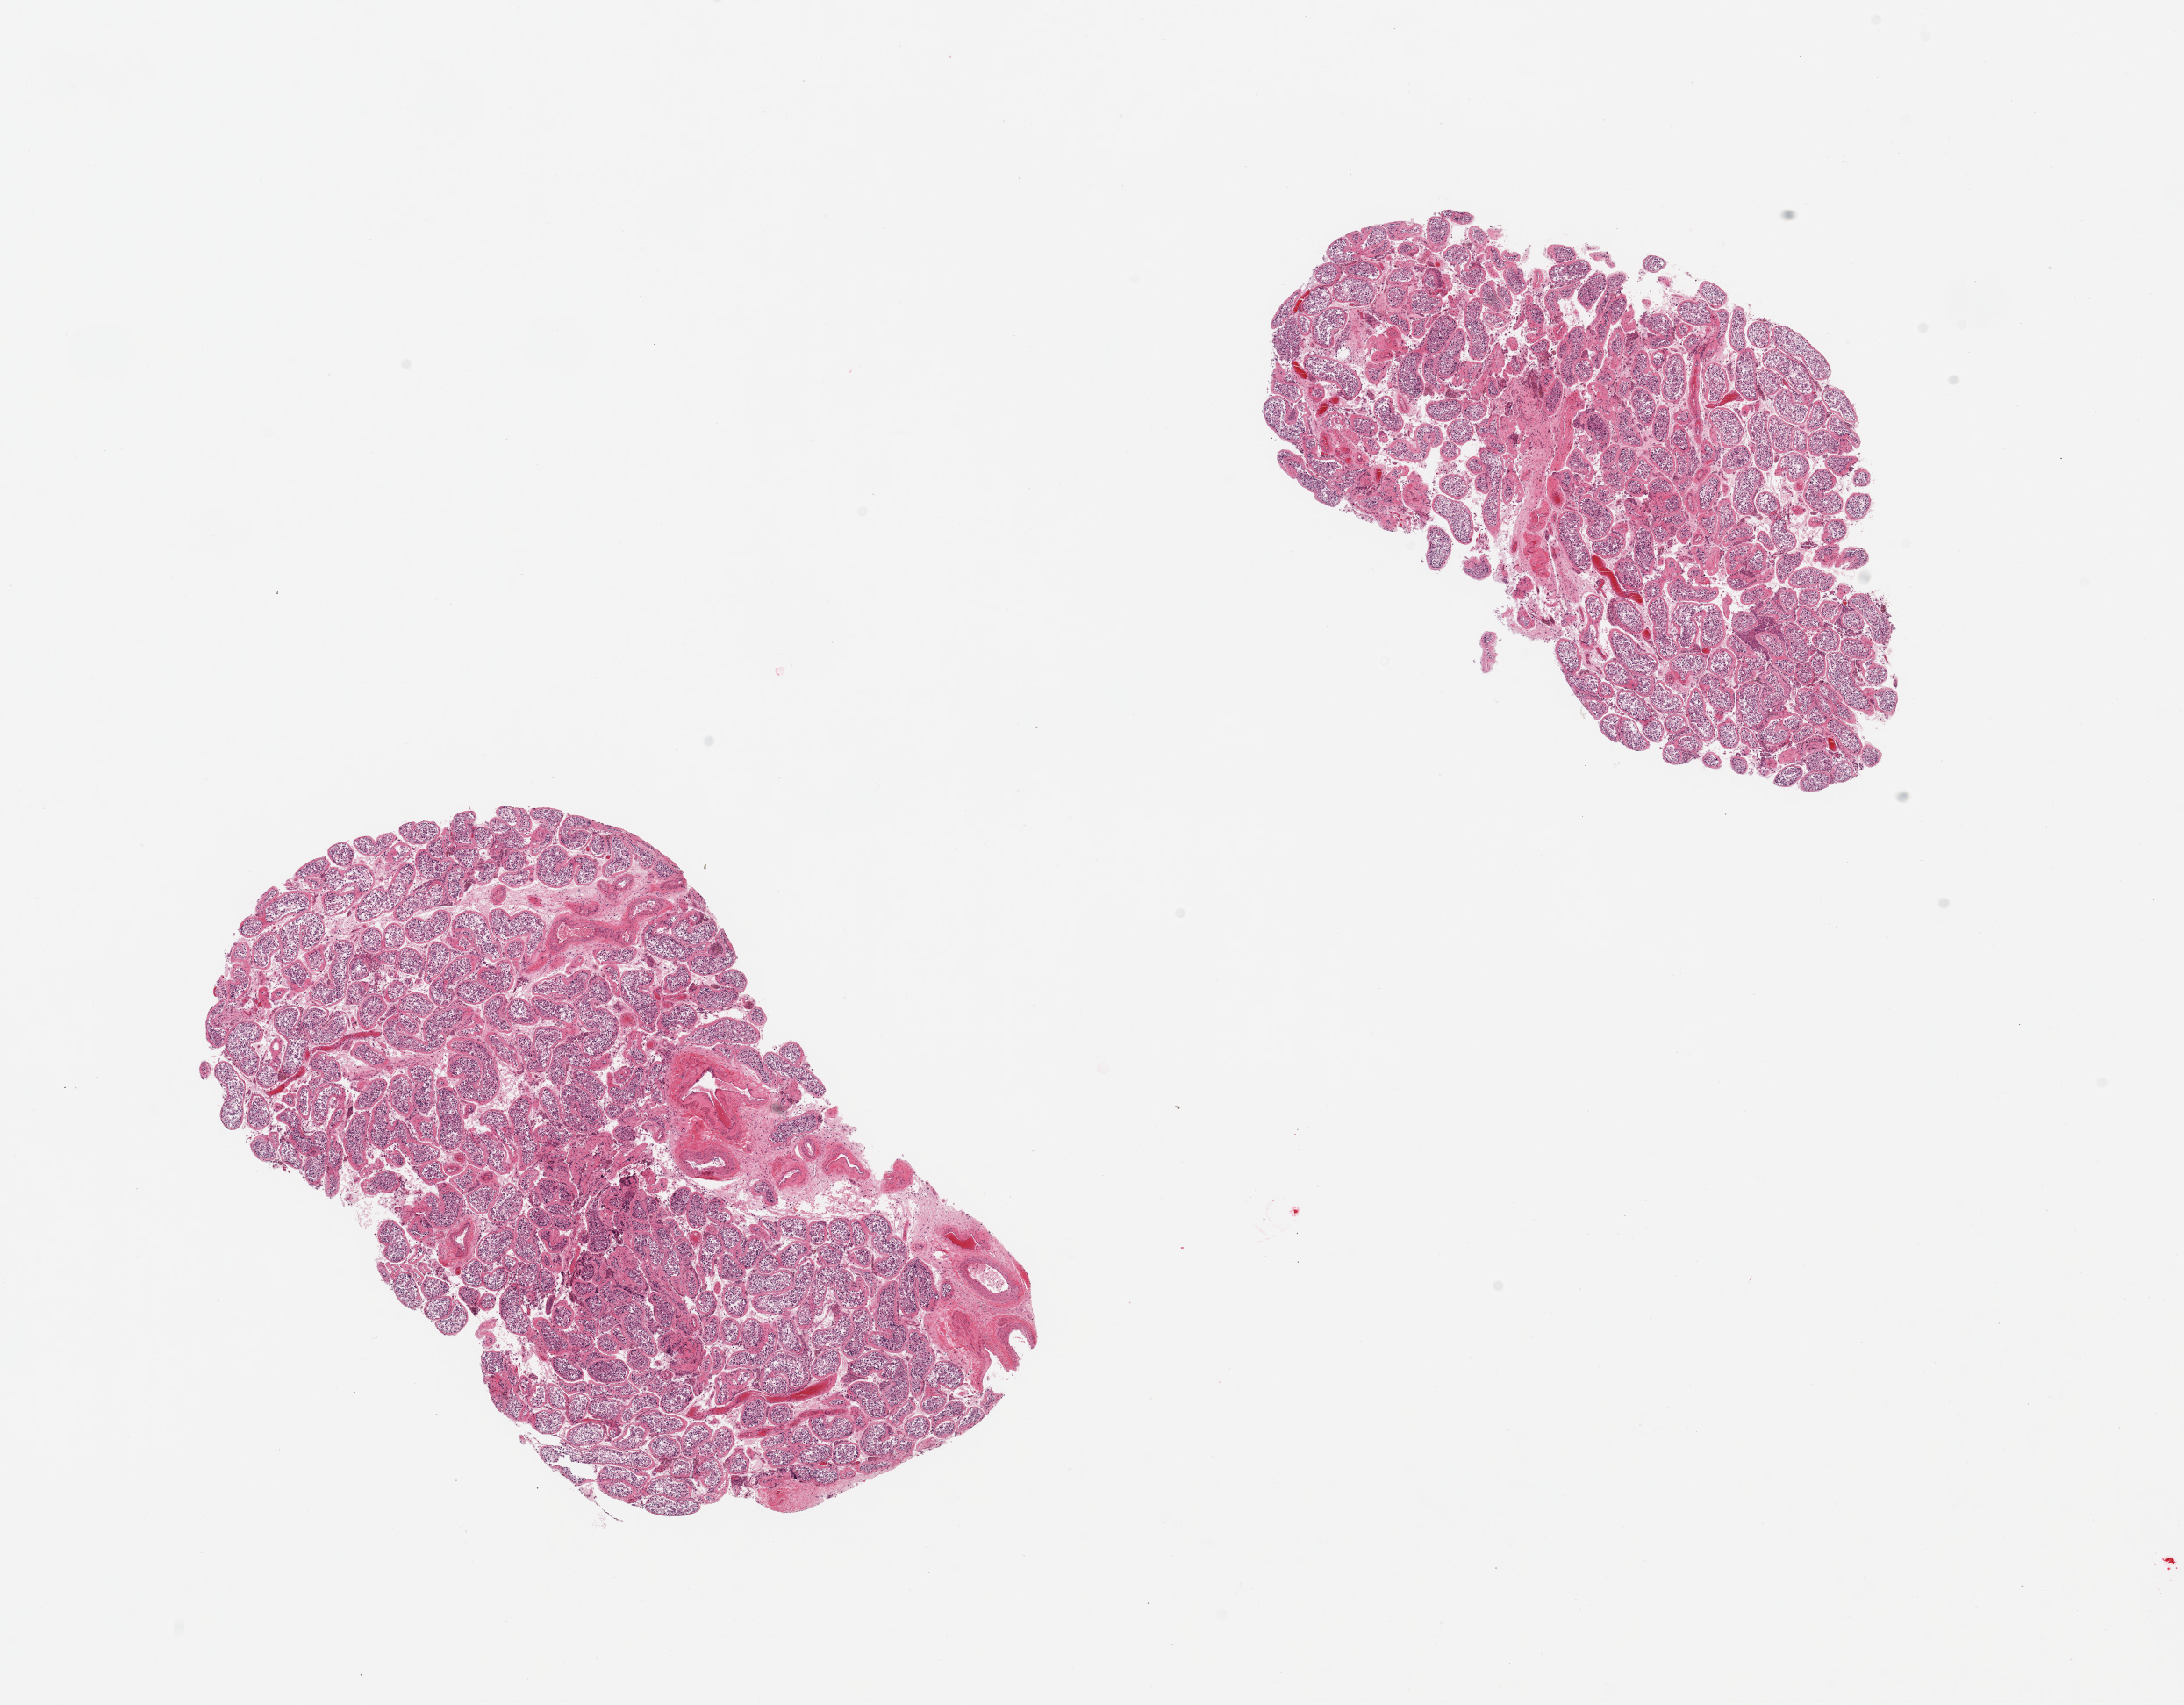
Digitized hematoxylin and eosin (H&E)-stained section, a low-resolution overview of the entire scanned area, about 19.7 x 15.4 mm, PAXgene-fixed, paraffin-embedded tissue, target tissue: testis, donor tissue sample. Male donor.
Reviewer comment on this tissue sample: 2 pieces; spermatogenesis.